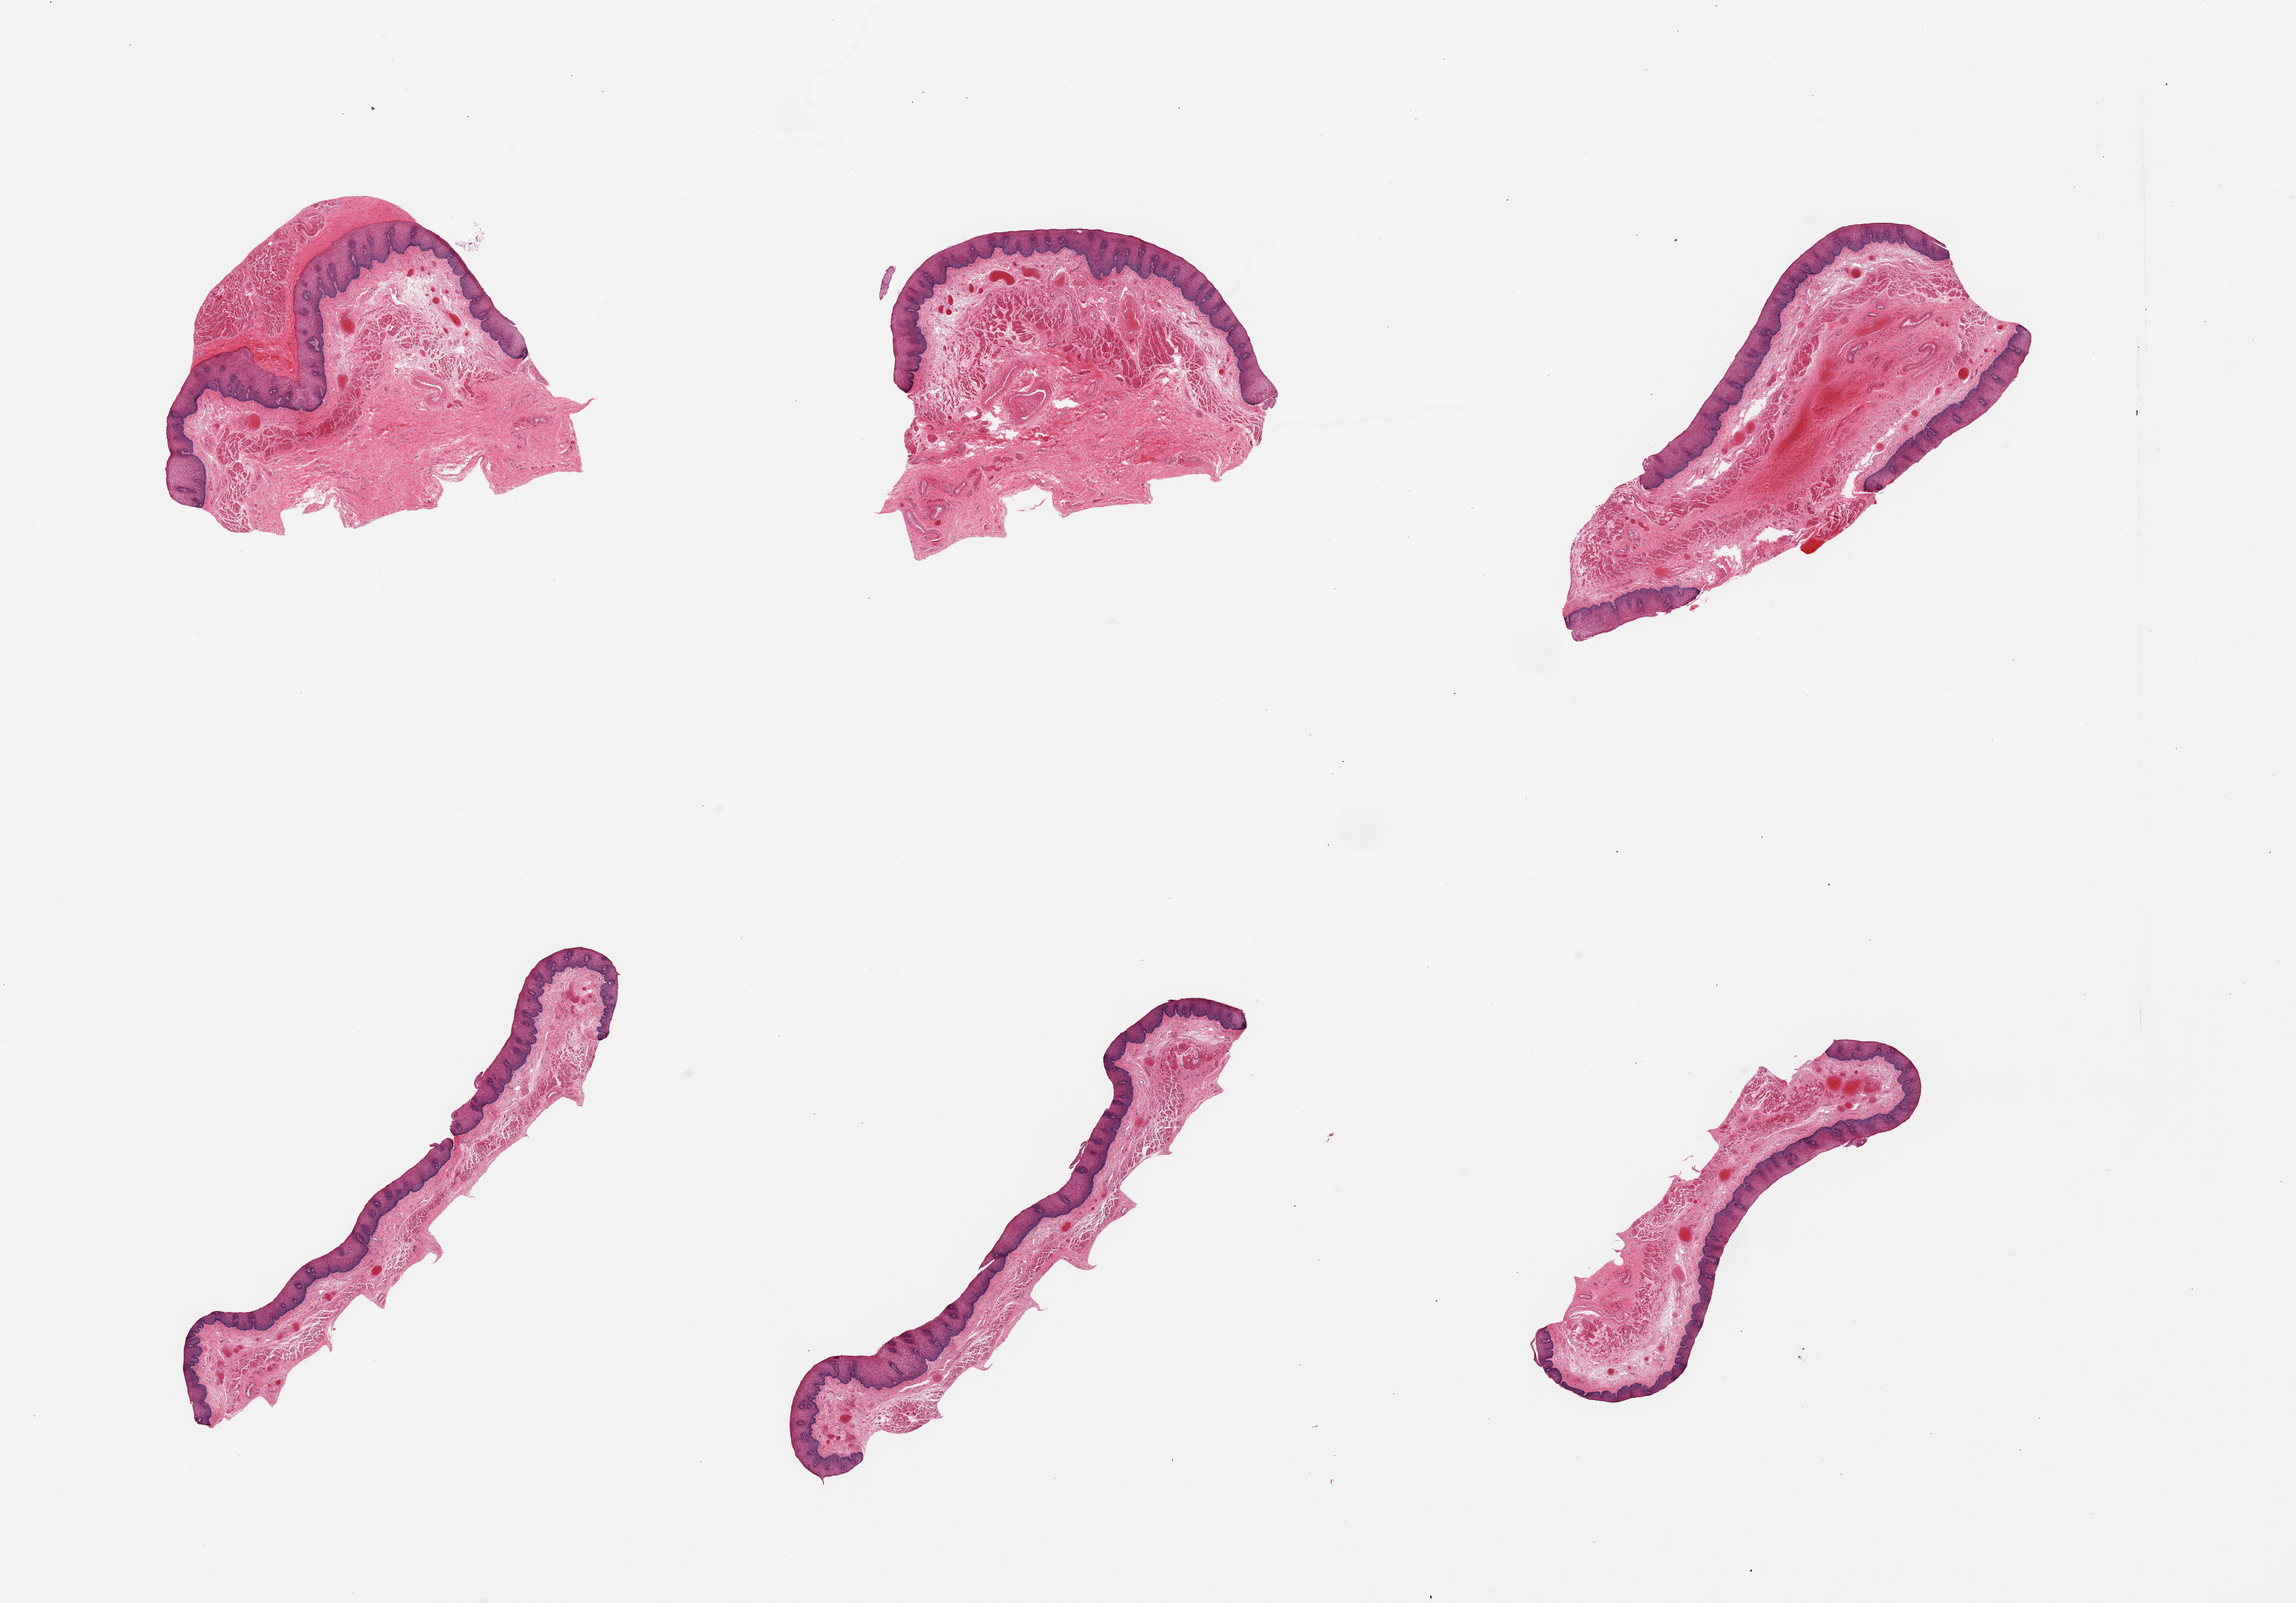
Digitized H&E-stained section — low-resolution overview of the scanned area, about 26.6 x 18.6 mm, PAXgene-fixed paraffin-embedded (PFPE) section, section of esophageal mucous membrane (target tissue), tissue donor sample. Donor sex: female.
Reviewer comment on this tissue sample: 6 pieces; congestion, squamous epithelium up to 0.3mm.